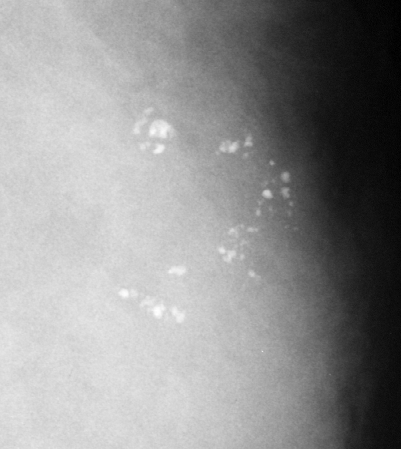
Crop from a digitized film mammogram around one marked abnormality, left breast, MLO view.
- Finding: calcifications, morphology pleomorphic, distribution clustered; BI-RADS assessment category 4; subtlety rating 5 on a 1 (subtle) to 5 (obvious) scale; pathology result (as recorded, not read from the image): benign.